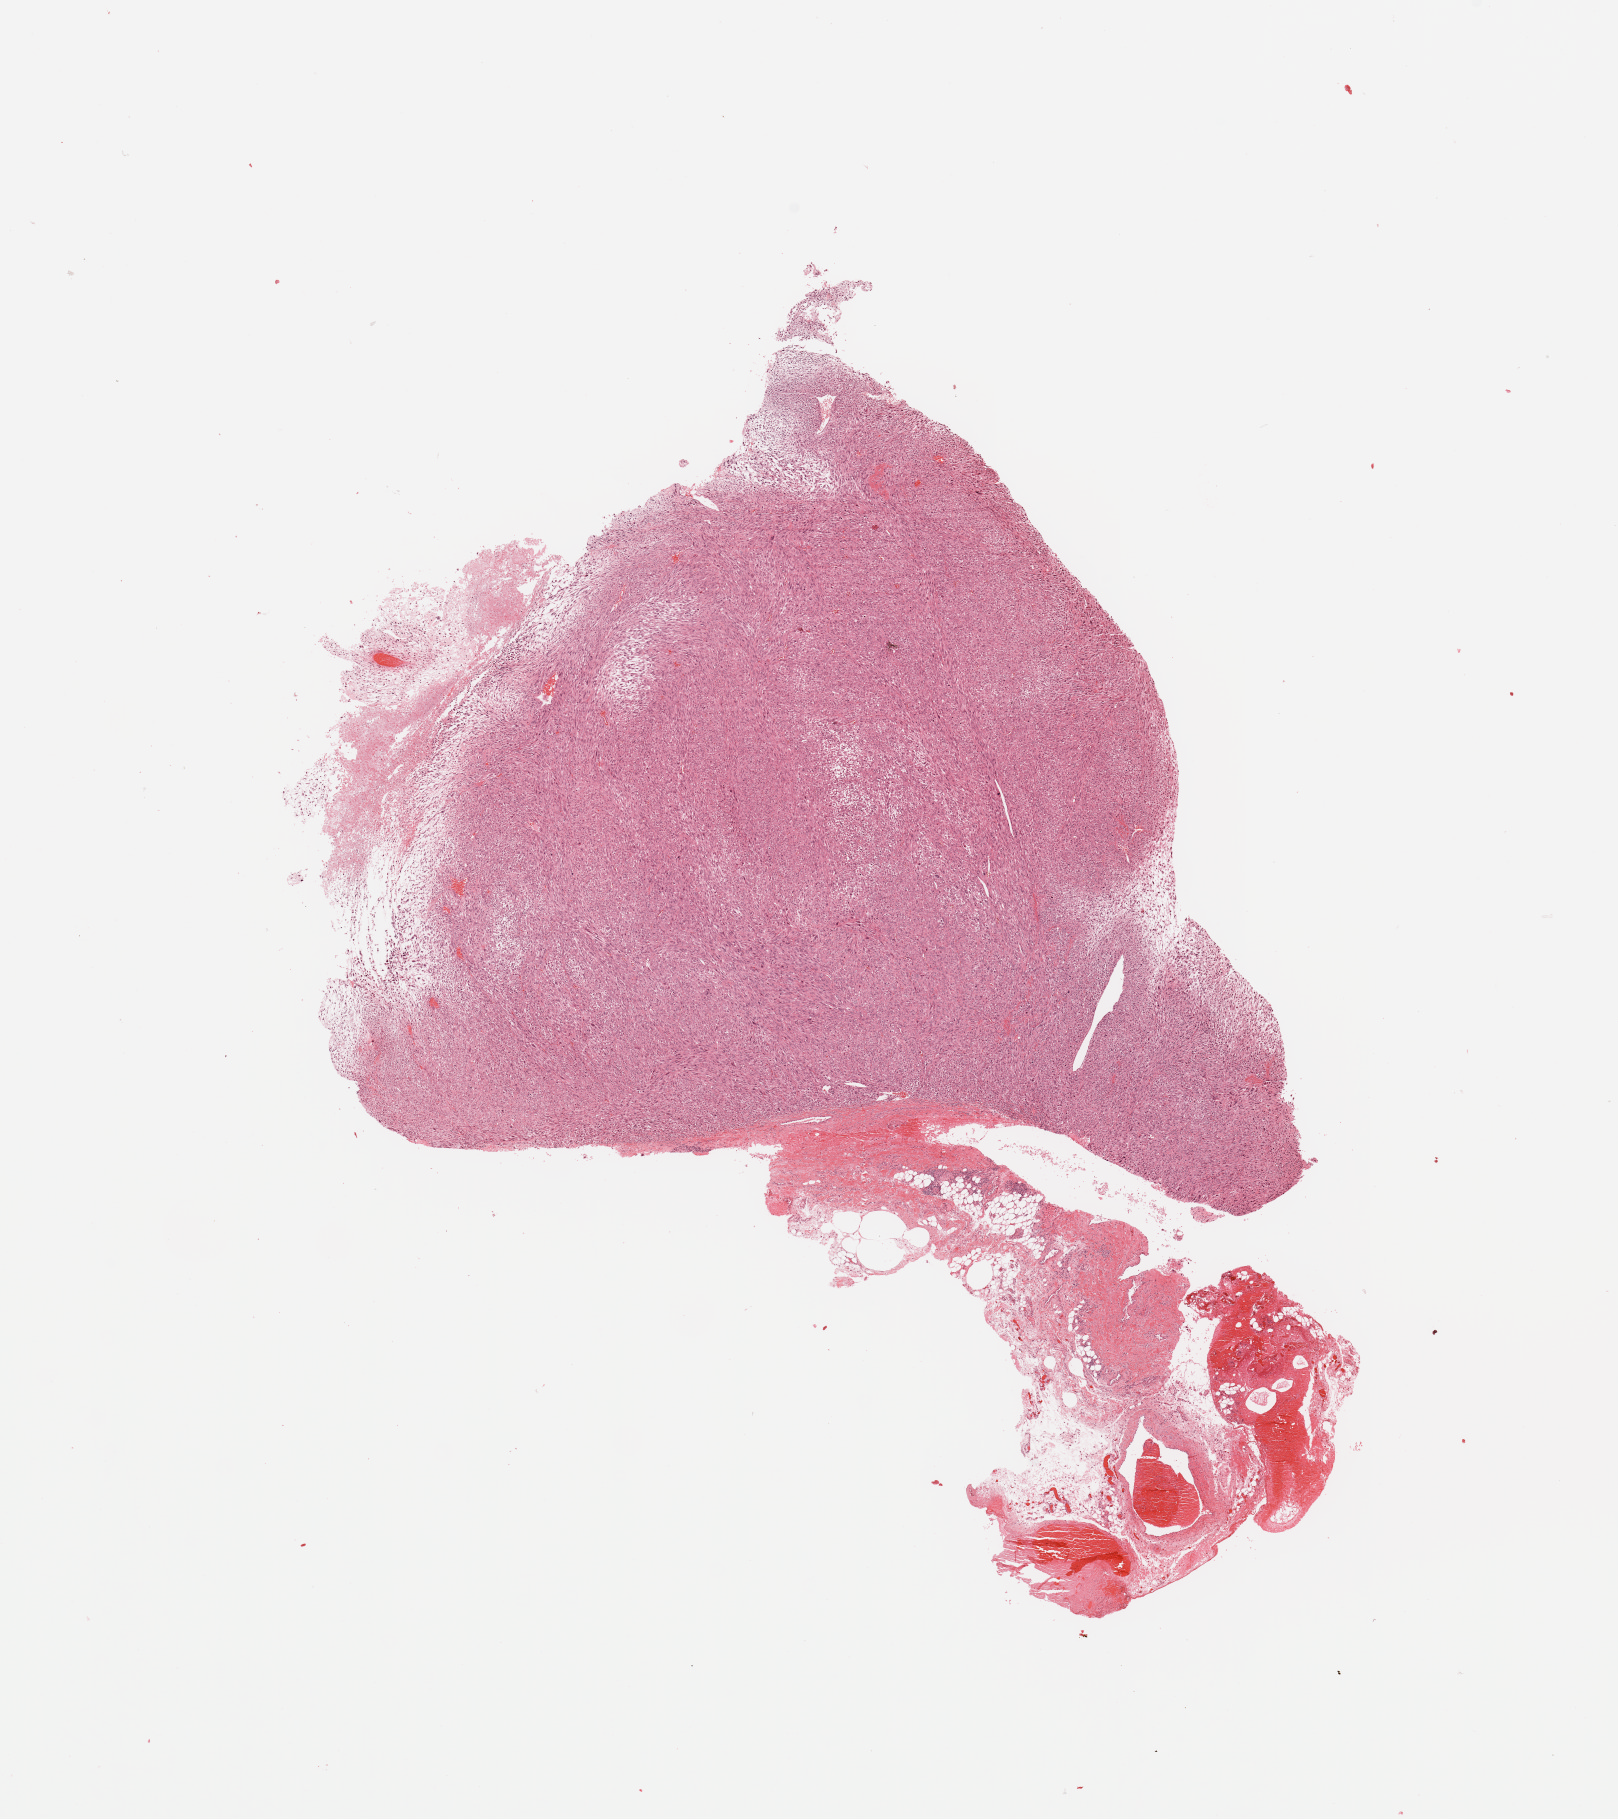
H&E-stained whole-slide image — low-resolution overview of the scanned area, about 12.8 x 14.4 mm. Tumour tissue sample. 75-year-old male patient.
Patient diagnosis (cohort enrolment): sarcoma (site not recorded at cohort level).